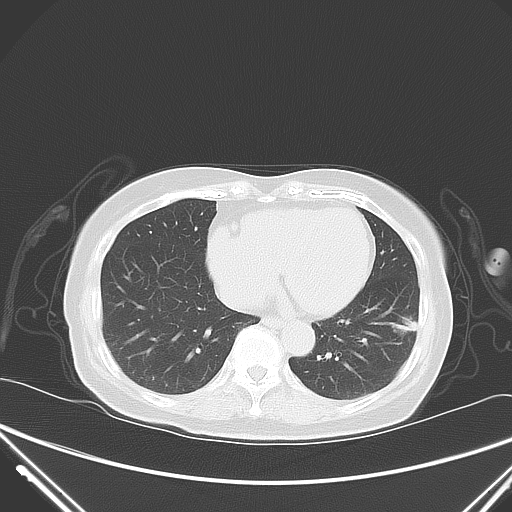
Chest CT, one axial slice; position 21 of 62 along the scan axis; 120 kVp; lung window (W 1500 / L -600 HU); 512 × 512 image matrix. Patient: female, 82 years. Case-level facts recorded for this patient, not image findings: clinical TNM (as recorded): T1c N0 M0; histopathological grade: G2.
Annotated regions visible in this slice (rectangle marked by the reading radiologist):
- lung tumour (recorded histology: adenocarcinoma): bounding box <381,302,416,351> (left, top, right, bottom; pixels)